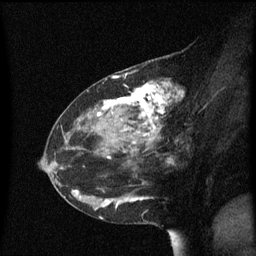
Breast MRI (dynamic contrast-enhanced), one sagittal slice. Dynamic contrast-enhanced series, image 2 of 3 at this slice position (ordered by acquisition). 1.5 T. TE 4.2 ms, TR 8.4 ms. 256 × 256 image matrix. Female patient, age 48 years. From the clinical record (not read from this slice): setting: breast cancer imaged before/during neoadjuvant chemotherapy; receptor status: HR-positive, HER2-negative.
Annotated regions visible in this slice (semi-automatically segmented with operator editing):
- analysis volume of interest (the breast-tissue region the enhancement analysis was run in; not a lesion): bounding box <80,78,193,221> (left, top, right, bottom; pixels)
- tumour enhancement mask (voxels above the 70 % enhancement threshold inside the analysis volume of interest): <98,83,183,209>